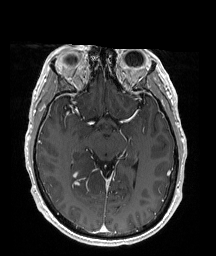
Brain MRI from a brain-tumour surgery series, one axial slice; position 107 of 176 along the scan axis; T1-weighted post-contrast; 1 mm slice thickness; 216 × 256 image matrix, field of view 211 × 250 mm. Case-level facts recorded for this patient, not image findings: histopathology: Oligodendroglioma; WHO grade: 2; IDH mutation: yes.
Structures marked on this image (expert manual segmentation):
- tumour: bounding box [x1, y1, x2, y2] px = [75, 150, 109, 205]